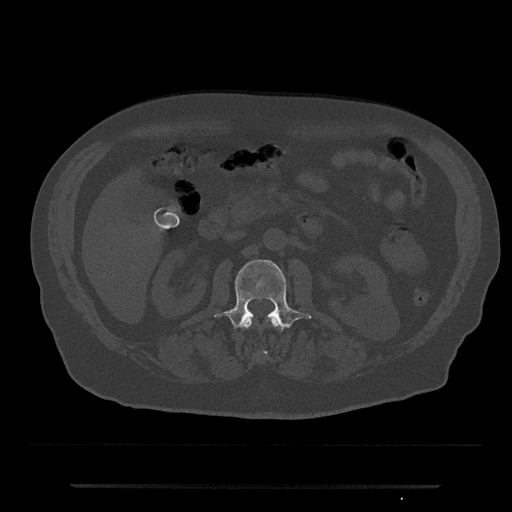
CT including the spine, one axial slice; position 485 of 797 along the scan axis; 120 kVp; bone window (W 1800 / L 400 HU); 512 × 512 image matrix, field of view 434 × 434 mm. Male patient, age 80 years. From the clinical record (not read from this slice): primary cancer: prostate; vertebrae with lytic lesions (as recorded): L1, T11.
Annotated regions visible in this slice (semi-automatically segmented with operator editing):
- L1 vertebra: bounding box (x1, y1, x2, y2) in pixels: (243, 317, 280, 354)
- L2 vertebra: (214, 259, 311, 331)